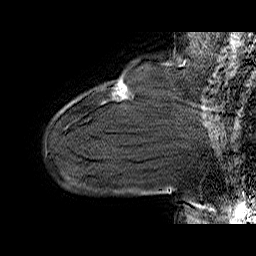
Breast MRI (dynamic contrast-enhanced), one sagittal slice. Dynamic contrast-enhanced series, time point 2 of 6 at this slice position (early post-contrast). 1.5 T. TE 6.4 ms, TR 32.9 ms. 4 mm slice thickness. 256 × 256 image matrix, field of view 200 × 200 mm. Female patient. Case-level facts recorded for this patient, not image findings: setting: breast cancer imaged before/during neoadjuvant chemotherapy; receptor status: HER2-positive.
Structures marked on this image (semi-automatically segmented with operator editing):
- analysis volume of interest (the breast-tissue region the enhancement analysis was run in; not a lesion): box from (x=114, y=77) to (x=130, y=99) px
- tumour enhancement mask (voxels above the 100 % enhancement threshold inside the analysis volume of interest): (x=118, y=84)–(x=127, y=89)